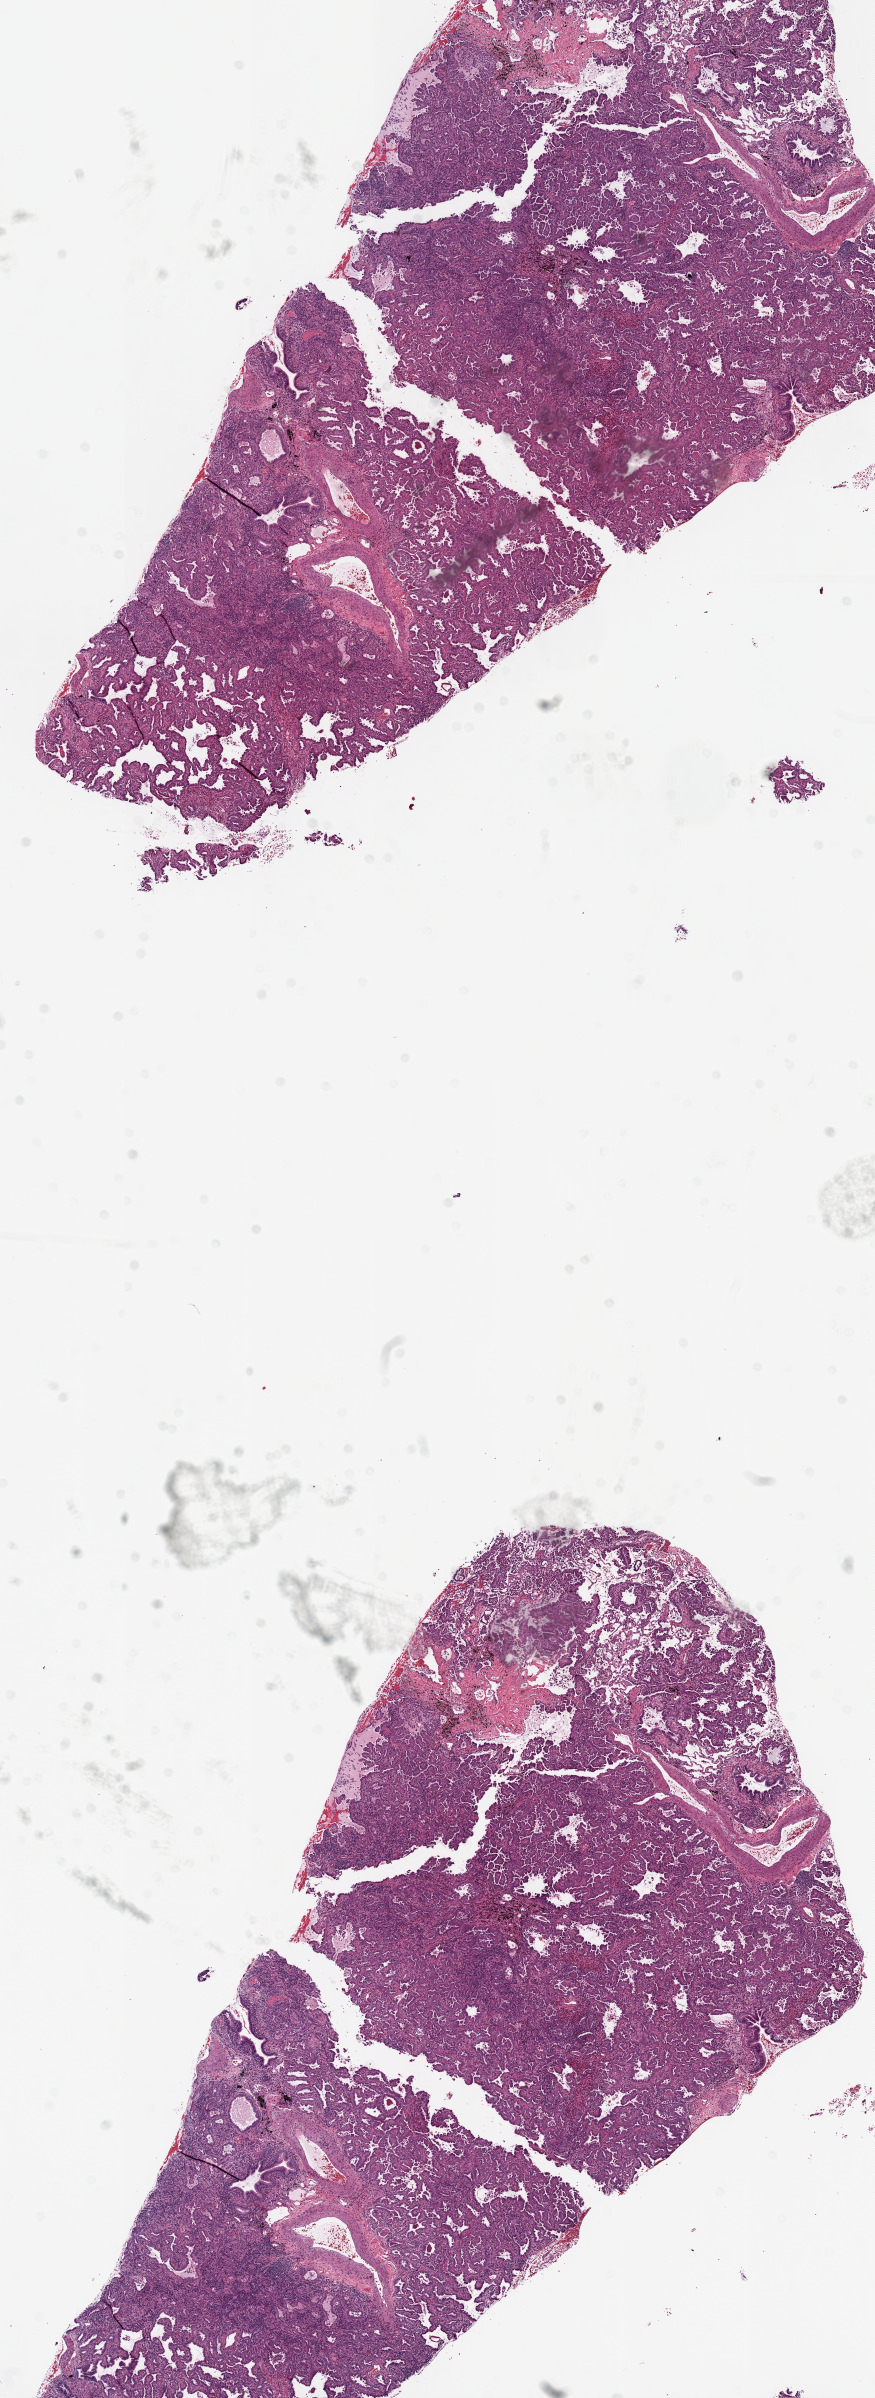
Digitized H&E tissue section (whole slide), whole scanned area (about 7.0 x 19.2 mm, from a 20x scan) shown as a low-resolution overview. Frozen section from the top of the tissue portion. Lung, primary tumour sample. Male patient; age at initial diagnosis 43 years. Slide review estimates, as recorded: tumour cells 88%, tumour nuclei 85%, normal cells 0%, stromal cells 12%, necrosis 0%. Infiltration values recorded for this section: lymphocyte infiltration 5%.
Pathologic diagnosis: Adenocarcinoma, NOS. AJCC pathologic stage: IB (6th edition).